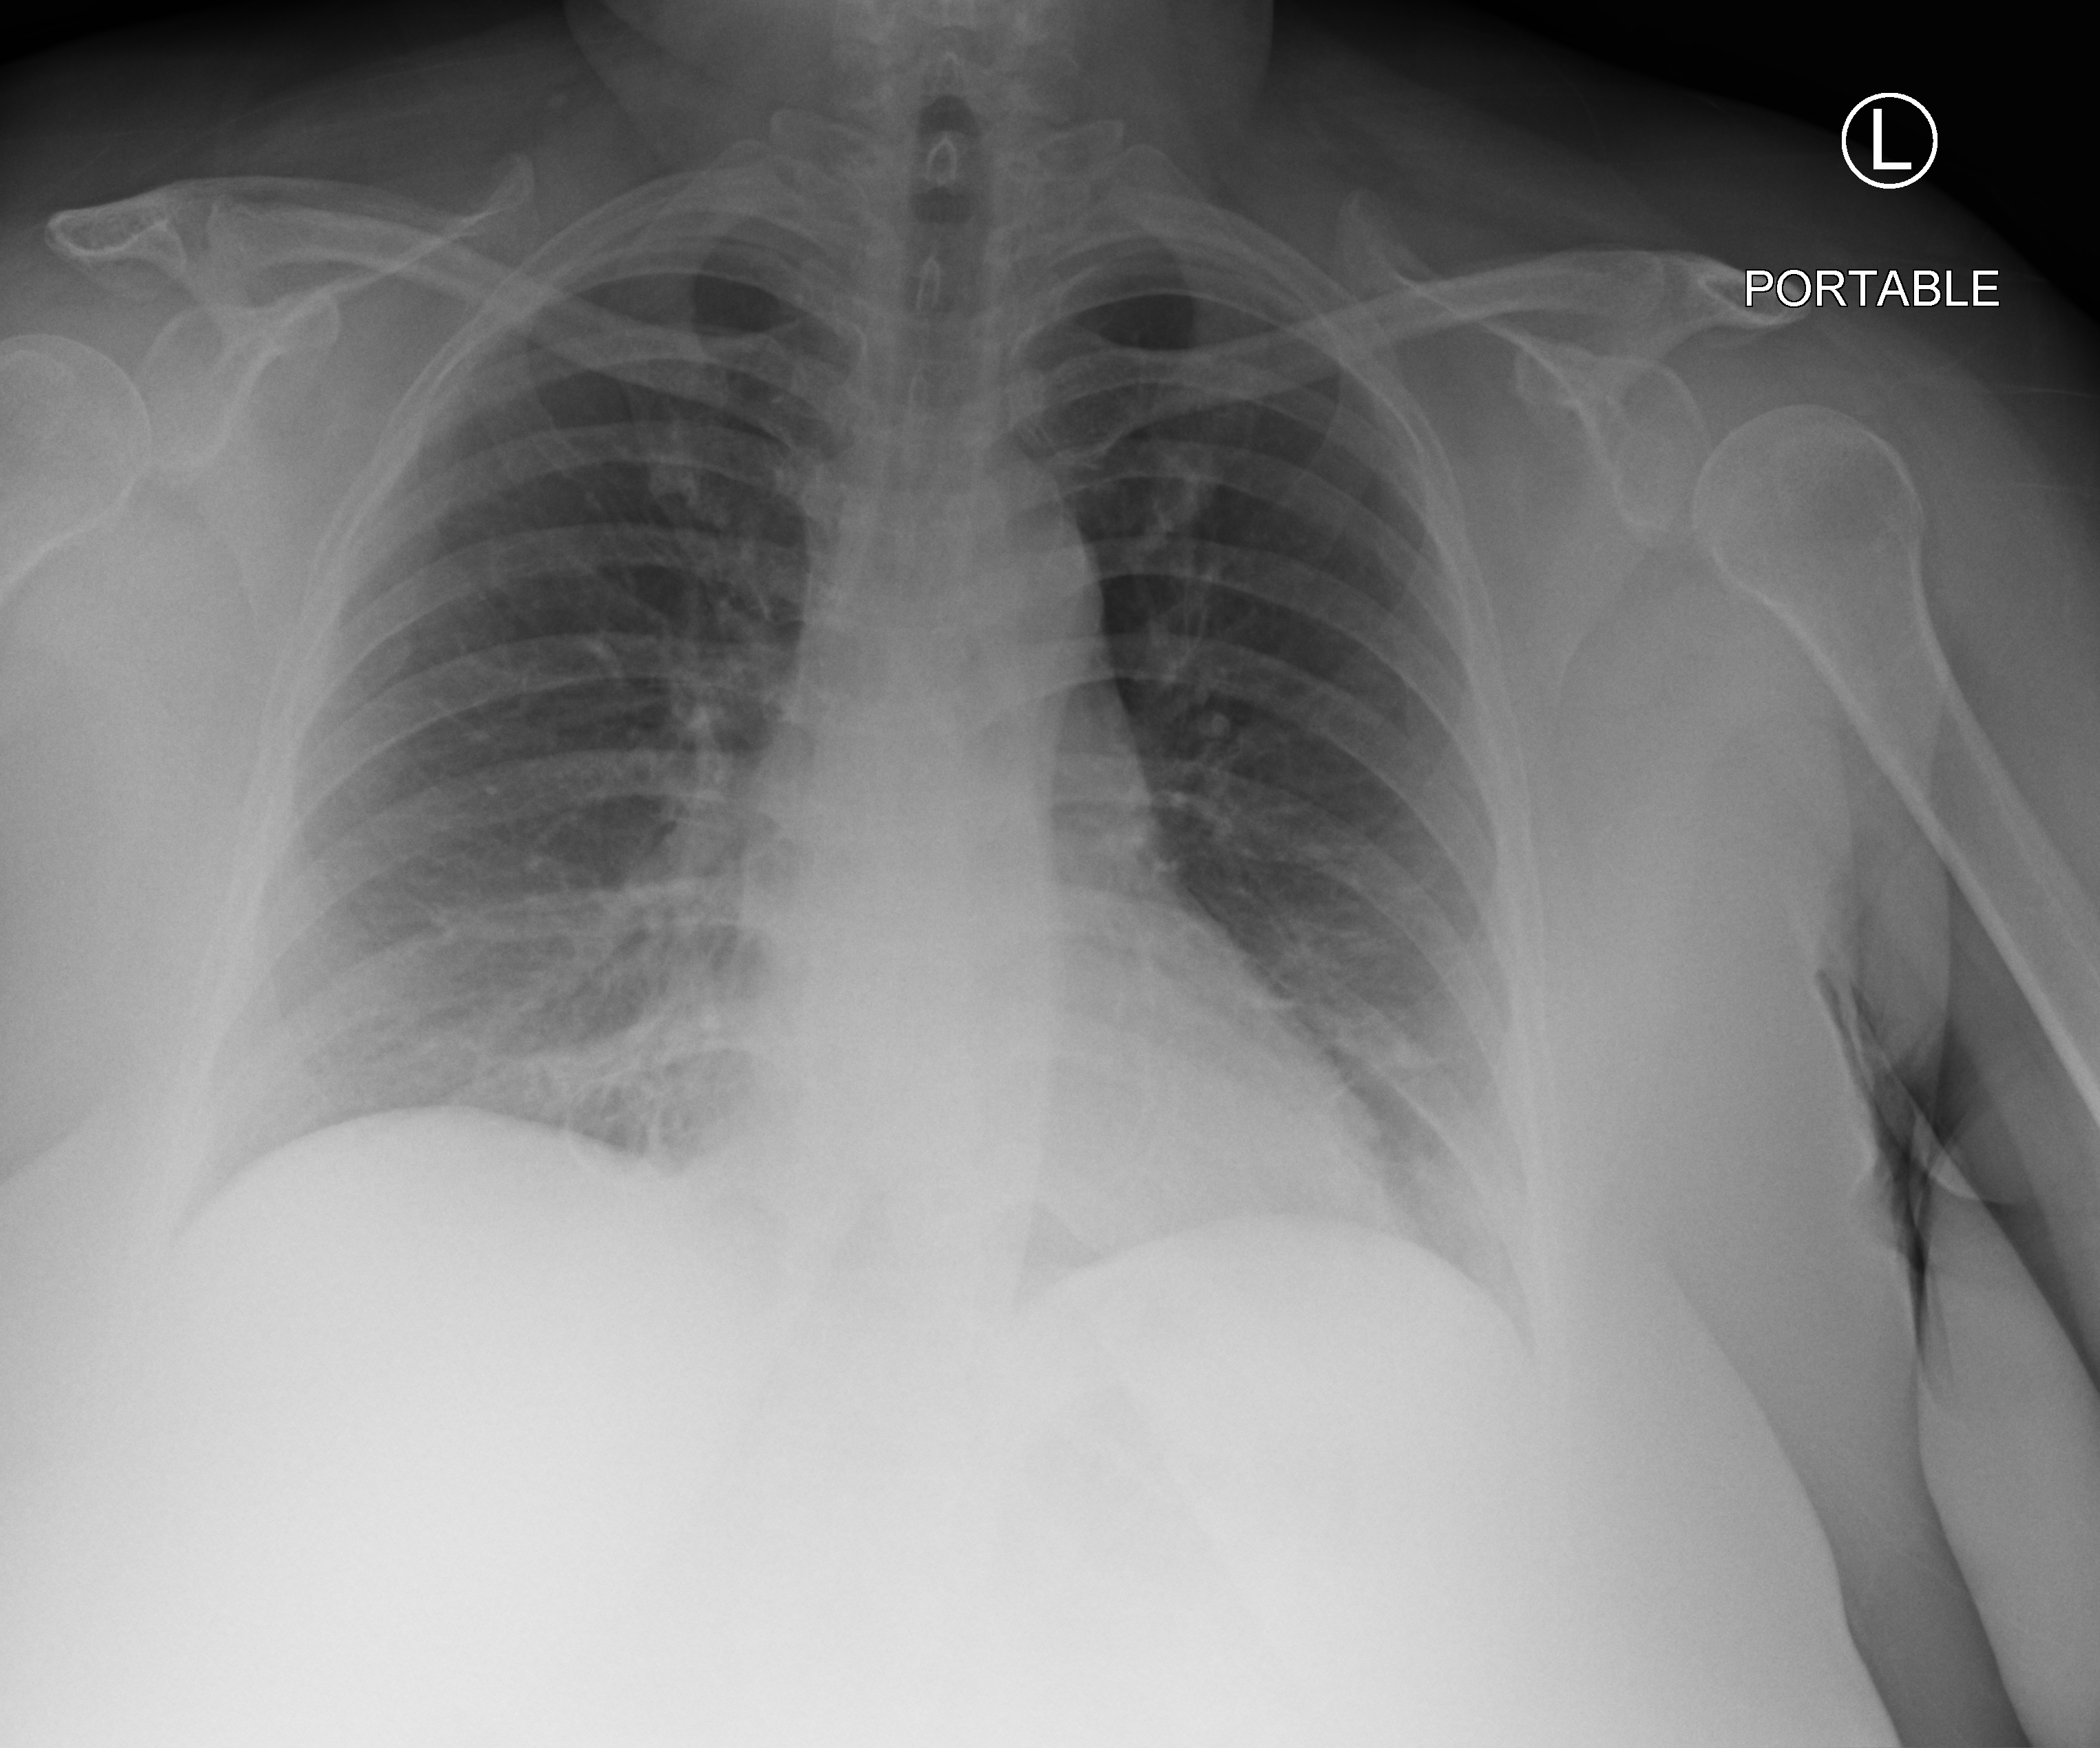
Chest X-ray (portable), anteroposterior (AP) projection. Female patient hospitalised with COVID-19, age 18–59 years.
Admission-level facts for this patient (not findings on this image; timing relative to this image not recorded):
- smoking status (admission record): former